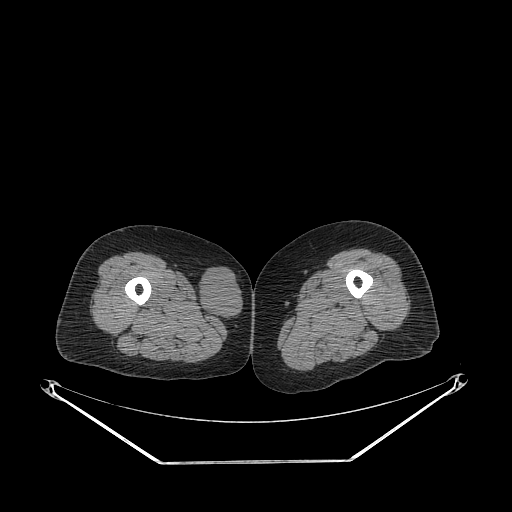
CT of an extremity soft-tissue mass (from a PET/CT study), one axial slice. Position 233 of 311 along the scan axis. Soft-tissue window (W 400 / L 40 HU). 3.75 mm slice thickness. 512 × 512 image matrix, field of view 500 × 500 mm. Female patient. Case-level facts recorded for this patient, not image findings: histological type: leiomyosarcoma; grade: intermediate; site of the primary tumour: parascapusular.
Annotated regions visible in this slice (expert contour drawn on MRI and transferred to this co-registered scan by the dataset authors):
- gross tumour volume including surrounding oedema: bounding box [x1, y1, x2, y2] px = [199, 267, 243, 321]
- gross tumour volume (mass): [199, 267, 243, 321]